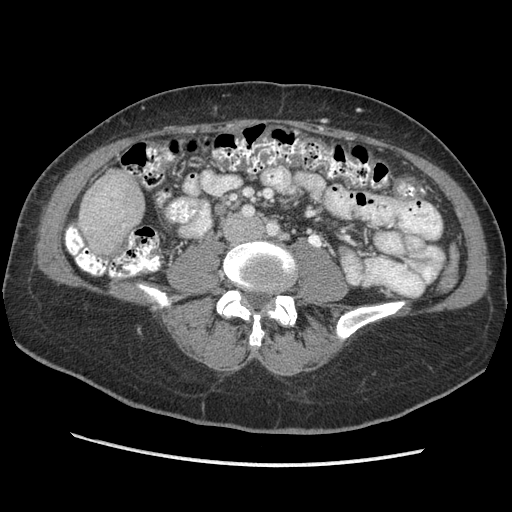
Contrast-enhanced abdominal CT (liver protocol), one axial slice. Slice 83 of 170 in the series (ordered by position). Reconstruction kernel STANDARD. Soft-tissue window (W 400 / L 40 HU). 2.5 mm slice thickness. 512 × 512 image matrix. Case-level facts recorded for this patient, not image findings: diagnosis: hepatocellular carcinoma (patient treated with transarterial chemoembolisation; whether this scan precedes or follows treatment is not stated here); TNM stage (as recorded): Stage-II; Child-Pugh class: A; tumour differentiation: no biopsy; tumour nodularity: multinodular.
Outlined on this slice (semi-automatic segmentation, software-assisted and operator-edited):
- liver parenchyma outside the tumour (the mass and vessels are separate outlines, so this box may not span the whole liver): box from (x=78, y=170) to (x=144, y=254) px
- liver vessels: (x=96, y=199)–(x=104, y=202)